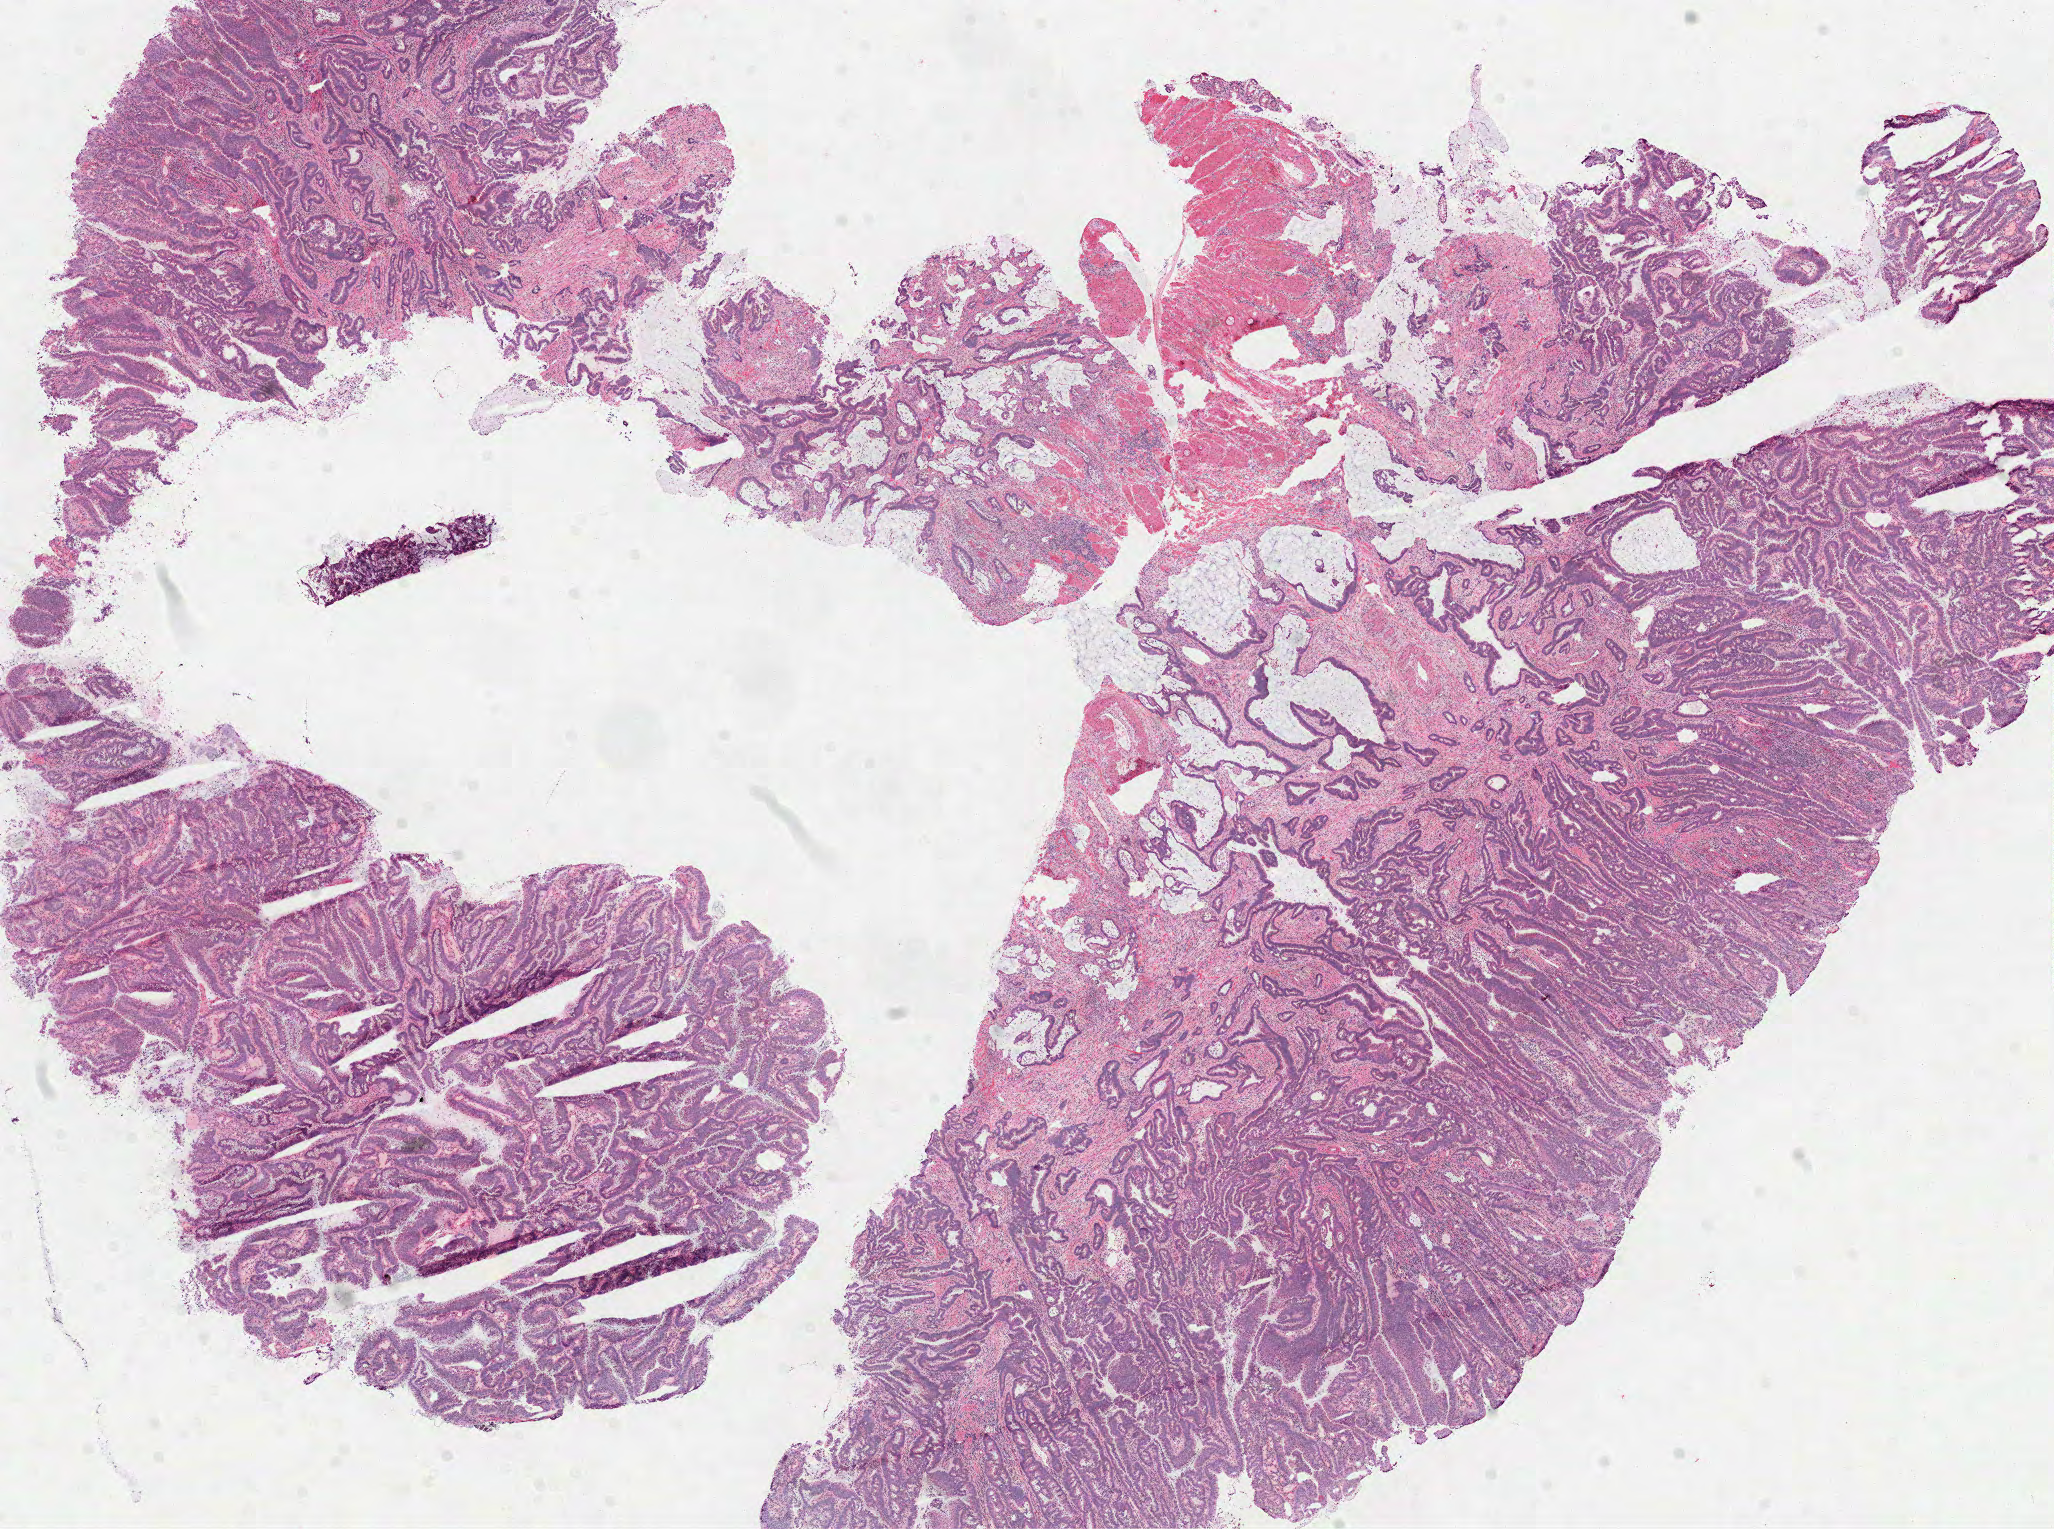
Hematoxylin and eosin (H&E) stained whole-slide image, whole scanned area (about 16.6 x 12.3 mm) shown as a low-resolution overview; frozen section from the top of the tissue portion; primary tumour sample from the colon. Patient: female, age at initial diagnosis 78 years. Composition of this section per pathologist review: tumour cells 85%, tumour nuclei 80%, normal cells 0%, stromal cells 15%, necrosis 0%.
Histologic diagnosis: Adenocarcinoma, NOS. AJCC pathologic stage: IIIB (7th edition).